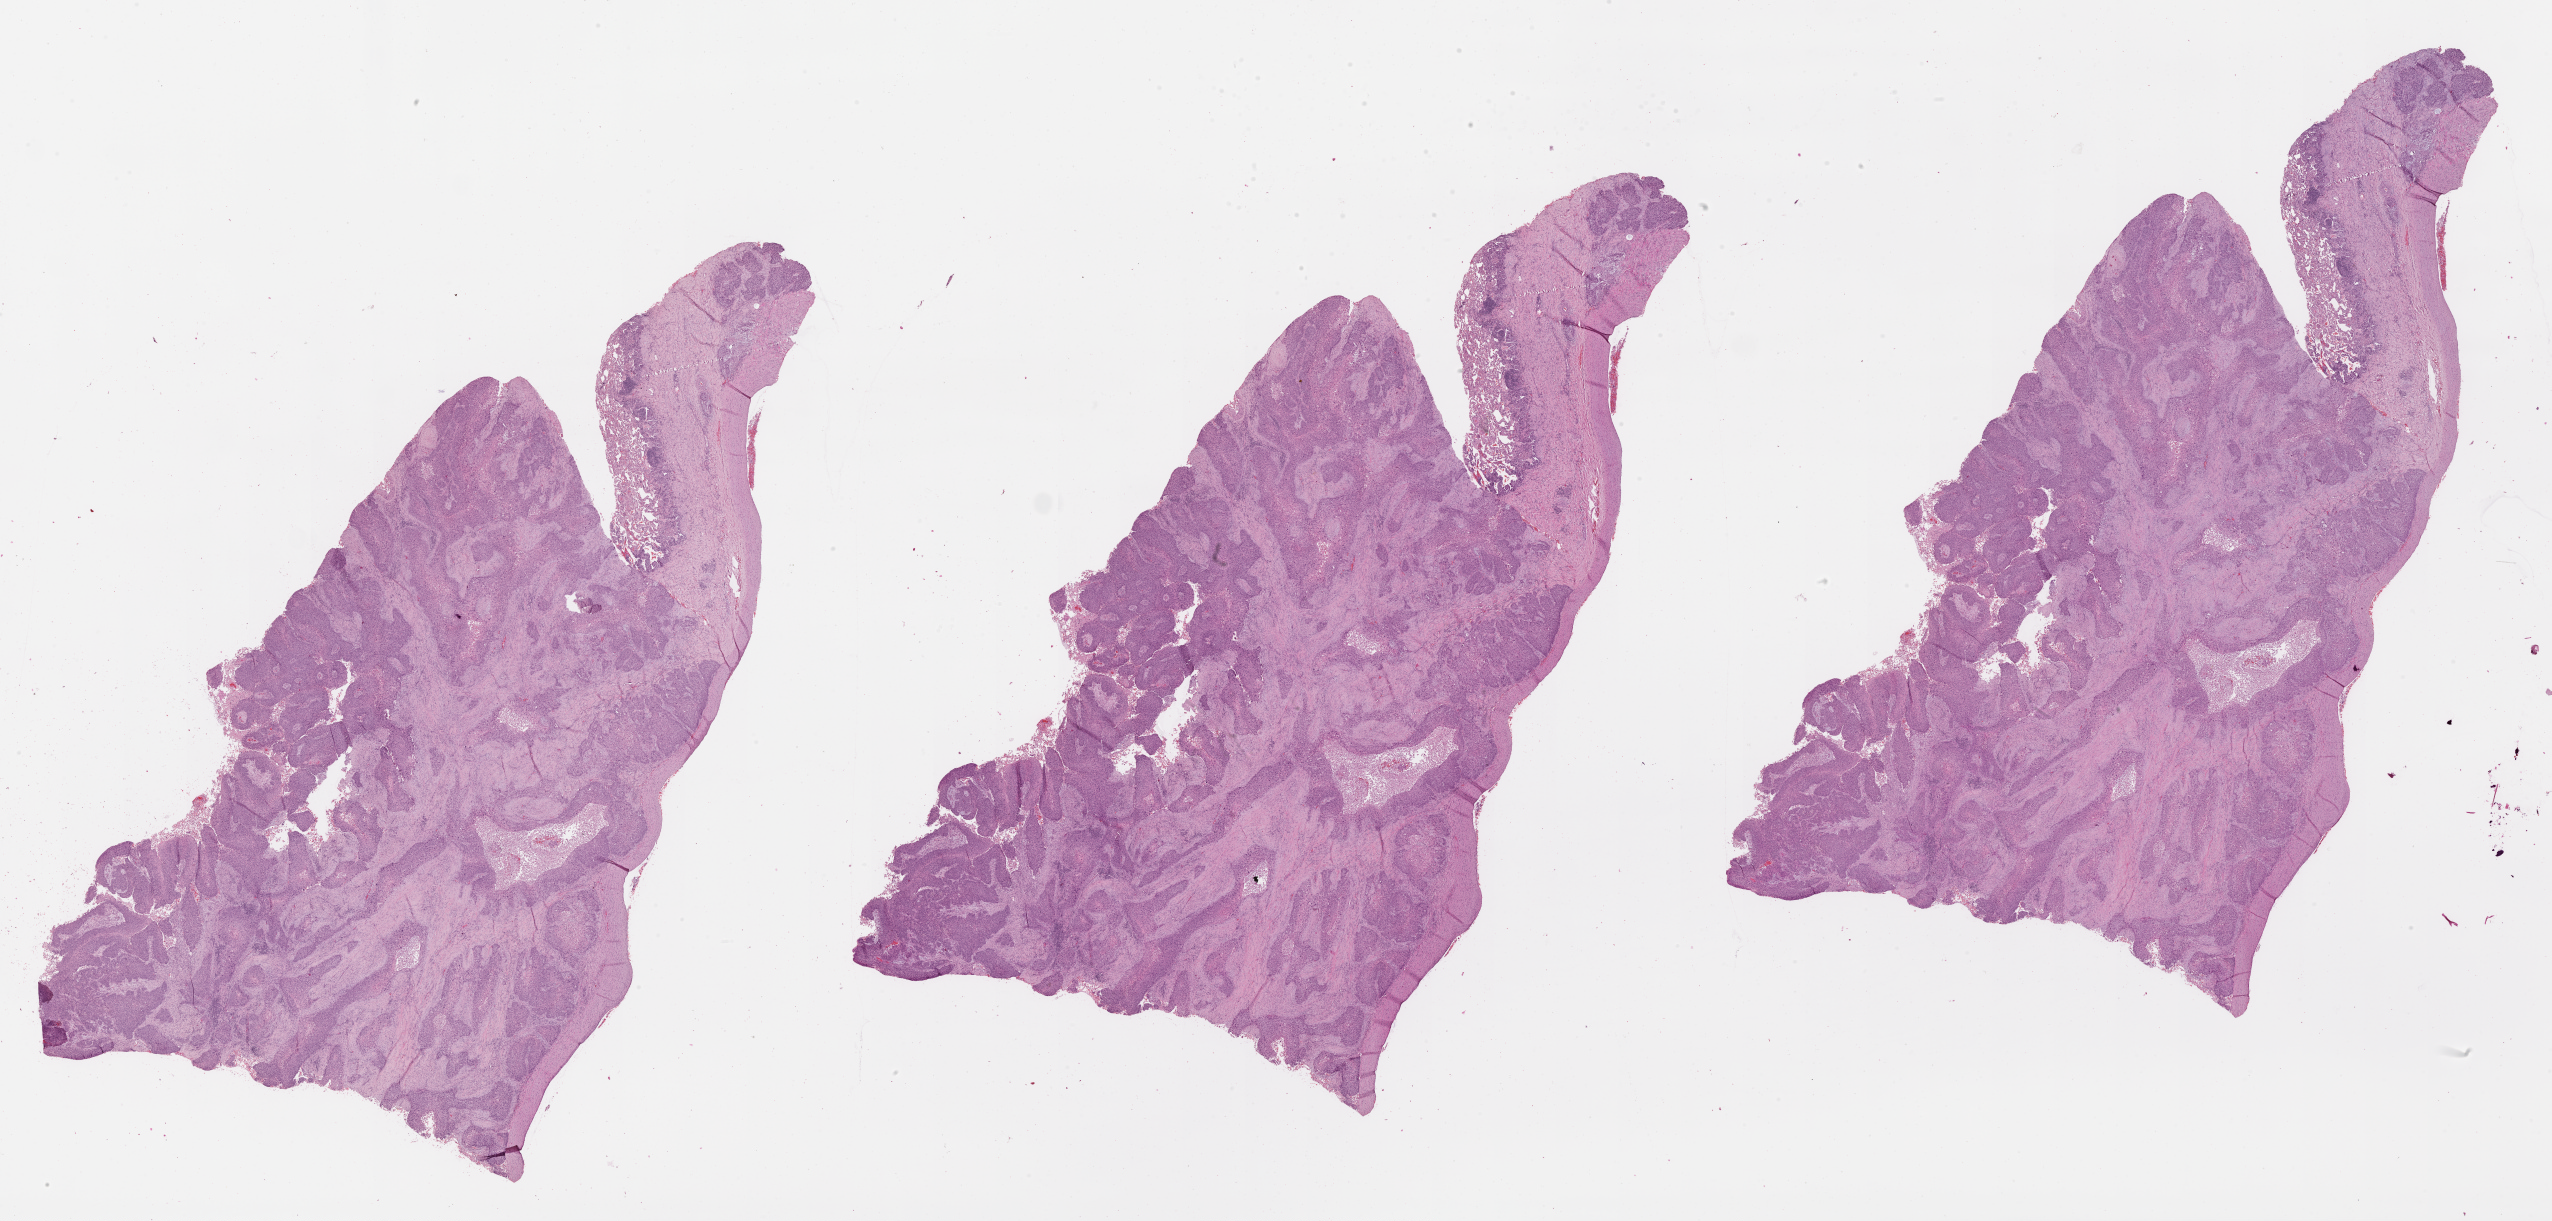
H&E whole-slide image — whole scanned area (about 41.1 x 19.7 mm, slide scanned at 20x) shown as a low-resolution overview; lung, tumour tissue. Patient: male, age 43 years.
Patient diagnosis (cohort enrolment): squamous cell carcinoma (lung).